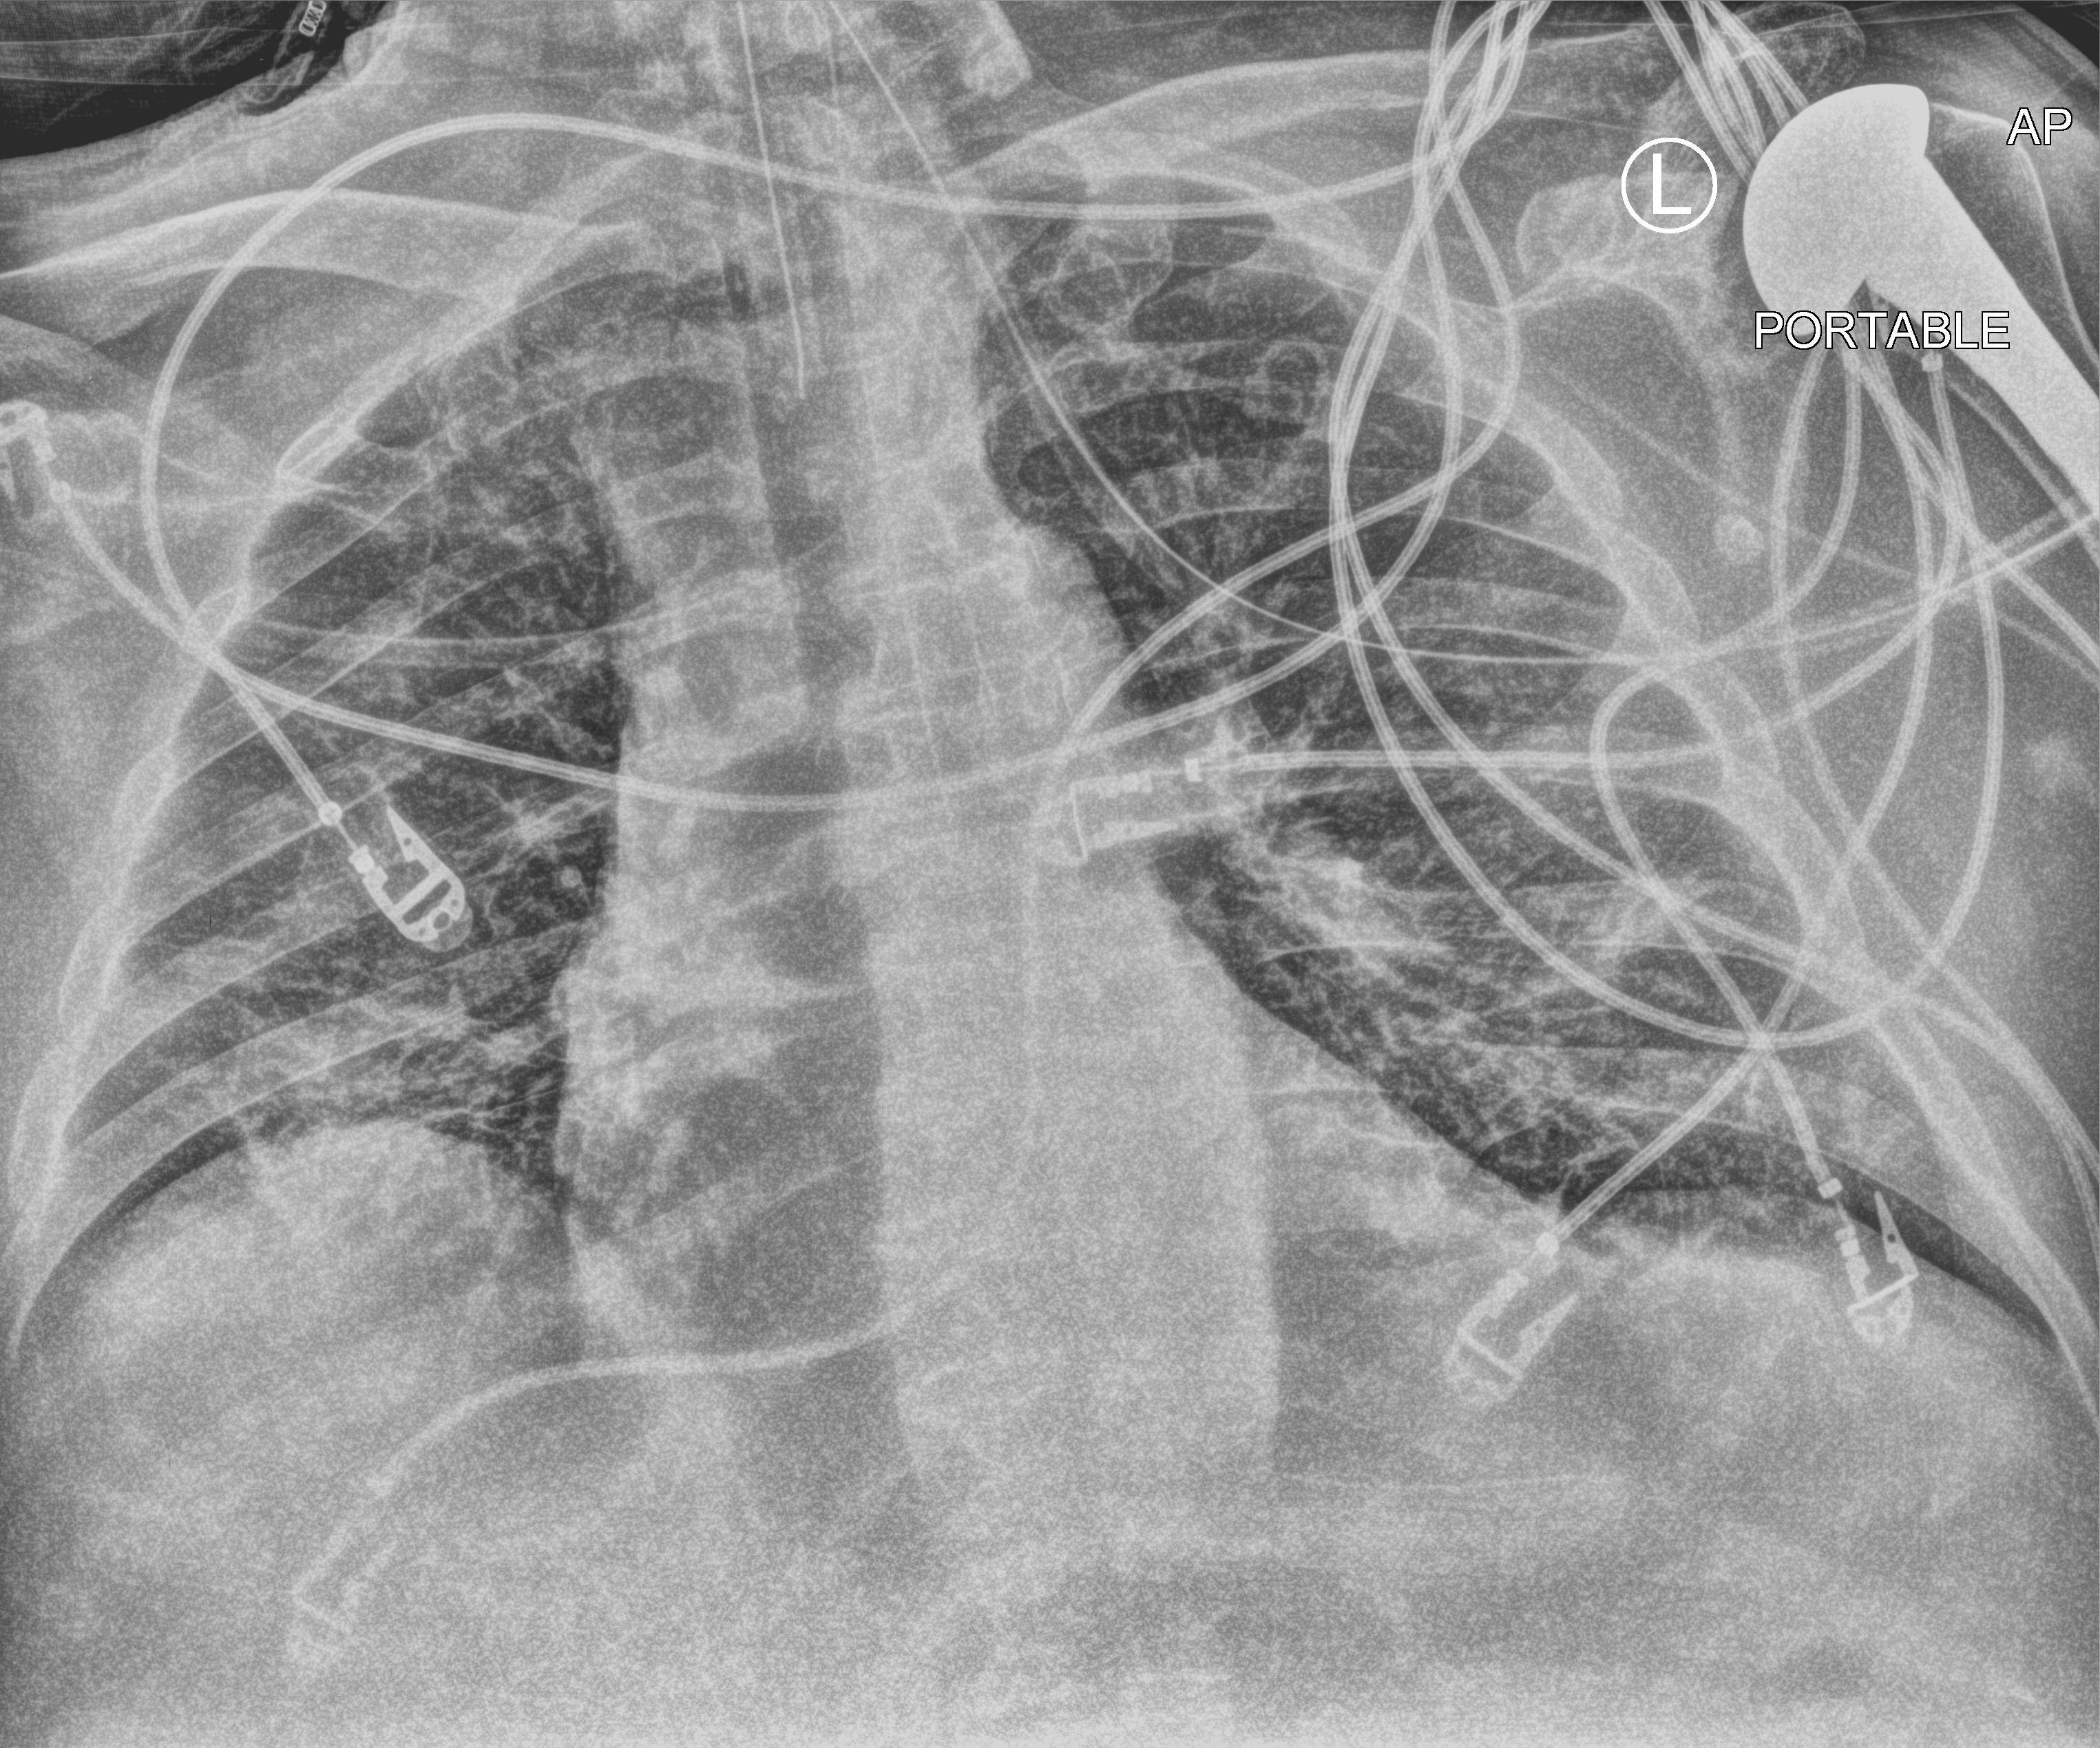
Bedside chest radiograph (computed radiography), anteroposterior (AP) projection. Male patient hospitalised with COVID-19, age 60–74 years.
From the hospital-stay record, not from the radiograph (when in the stay this image was taken is not recorded):
- mechanically ventilated during this hospital stay: yes
- admitted to intensive care during this hospital stay: yes
- length of hospital stay: 10 days